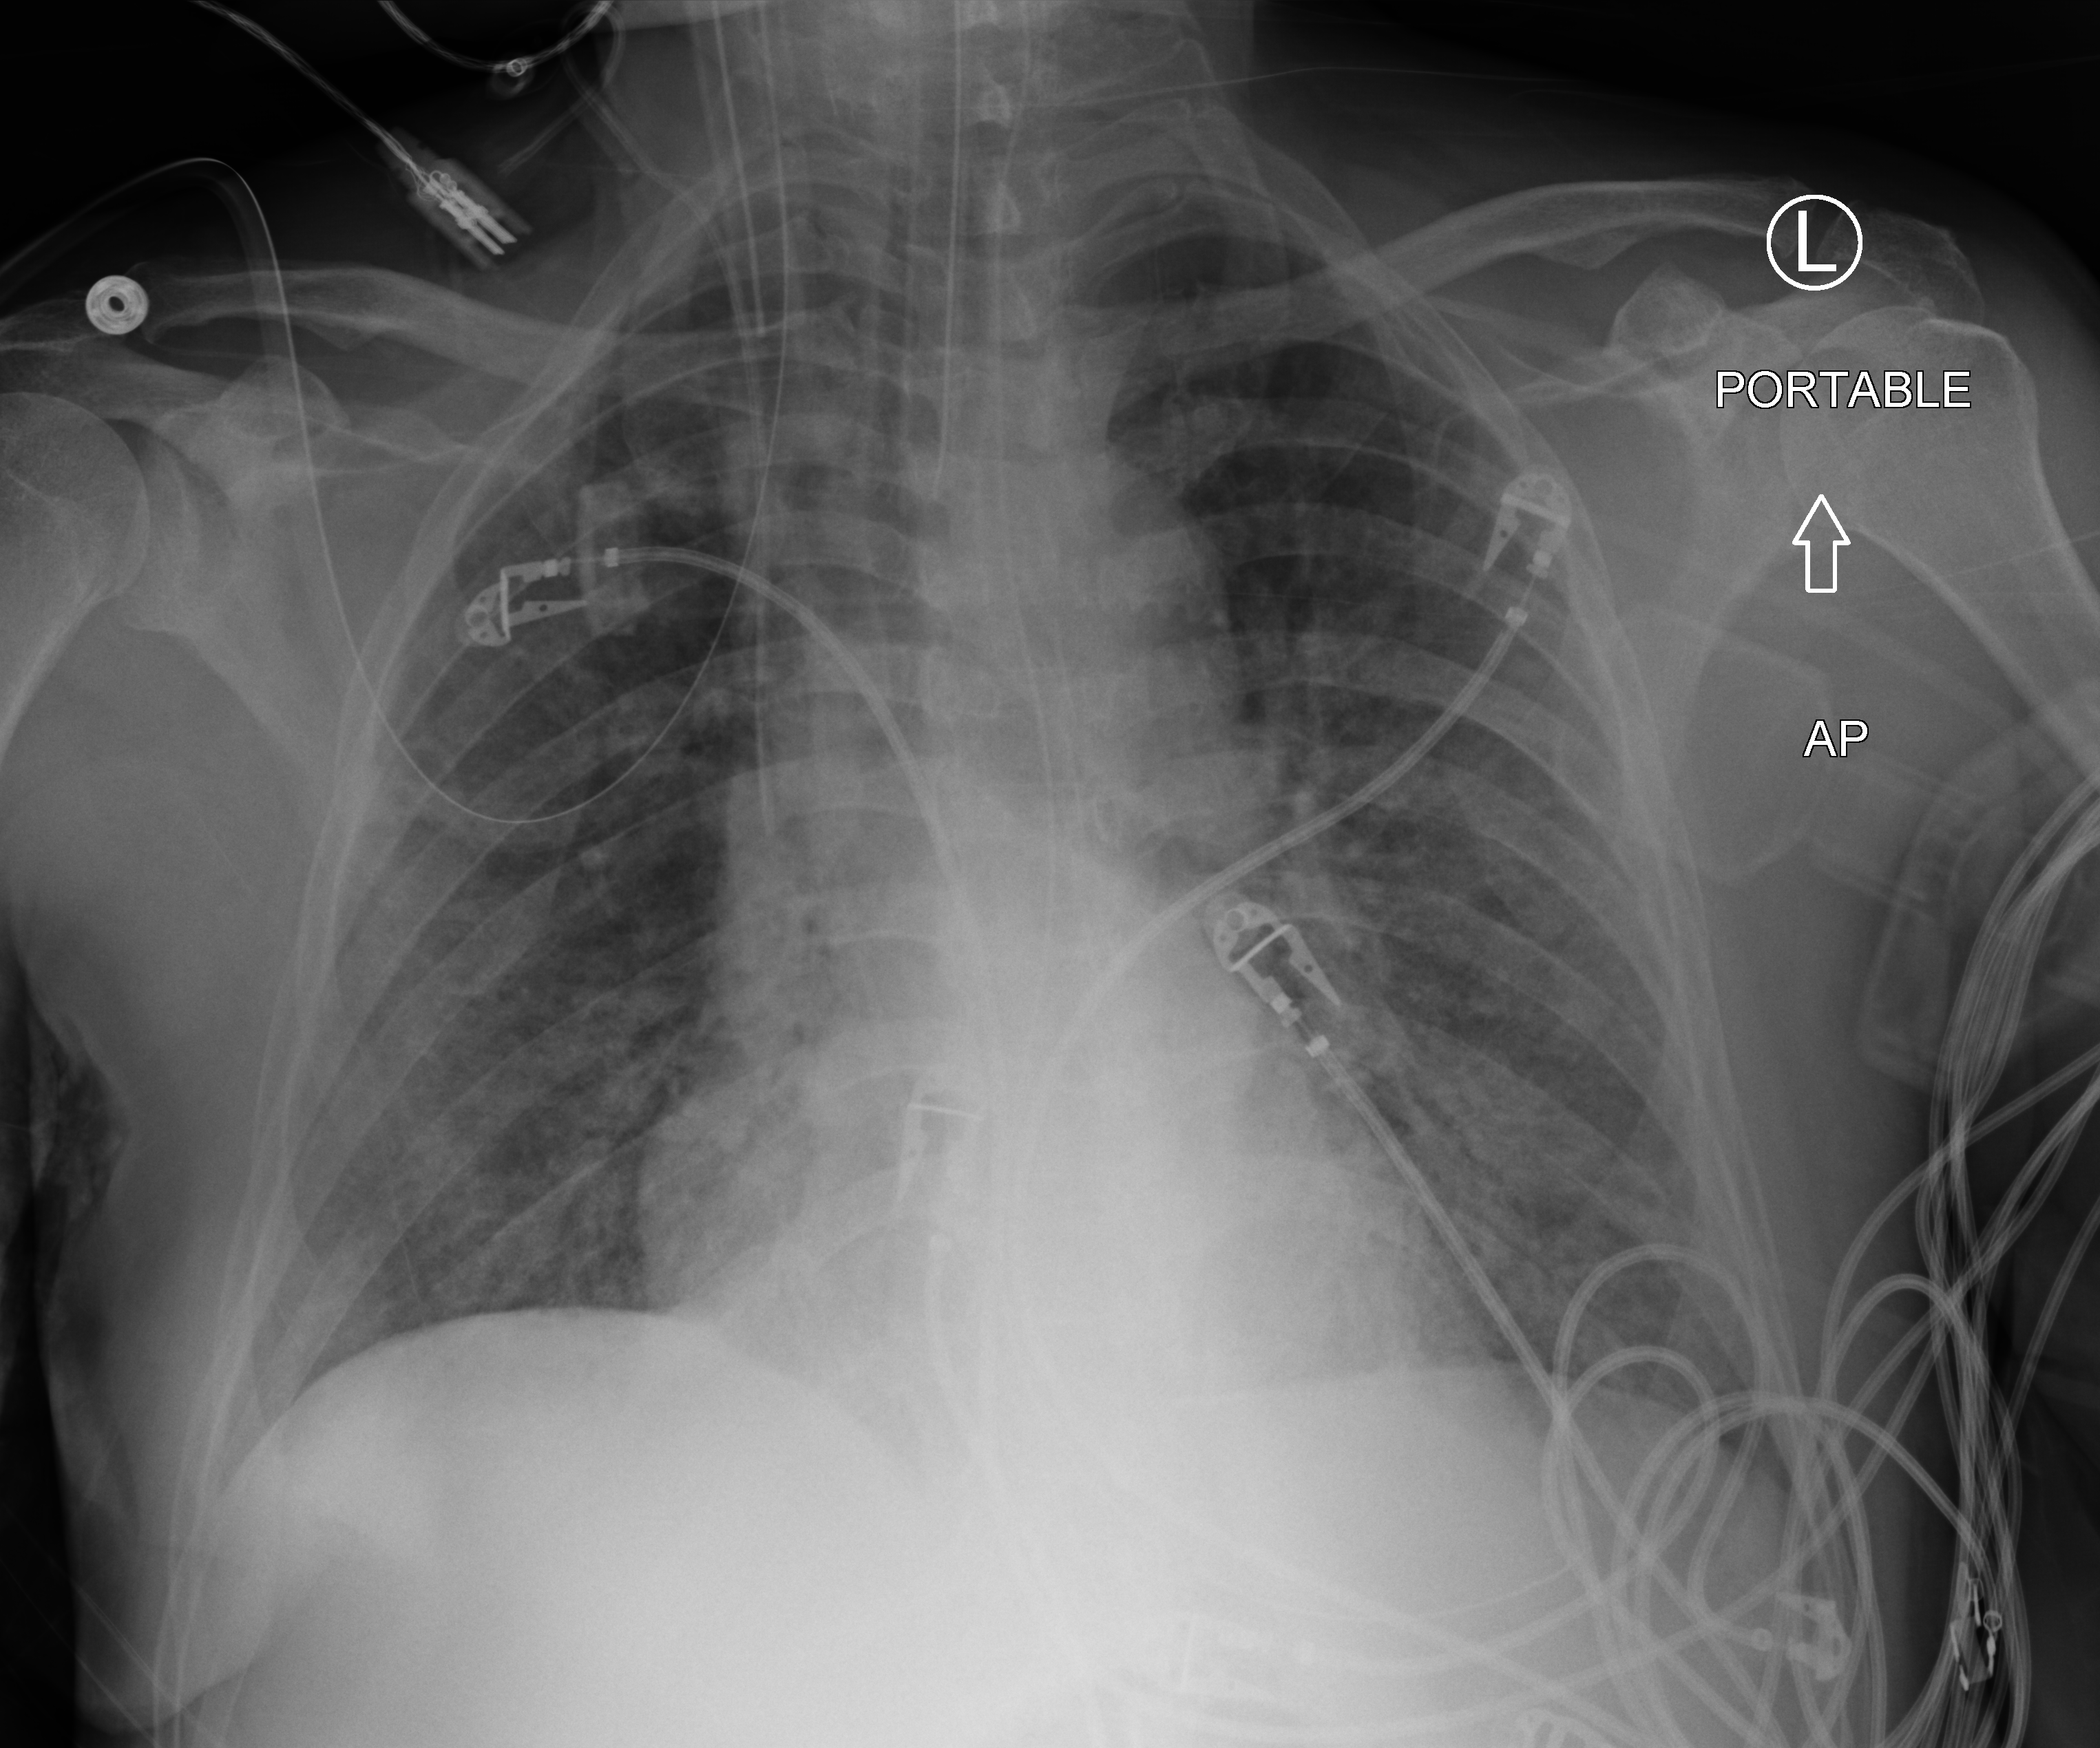
Portable chest radiograph, anteroposterior (AP) projection. Patient hospitalised with COVID-19; male, aged 60–74 years.
Admission-level facts for this patient (not findings on this image; timing relative to this image not recorded): chronic kidney disease (admission record): no; mechanically ventilated during this hospital stay: yes; admitted to intensive care during this hospital stay: yes.